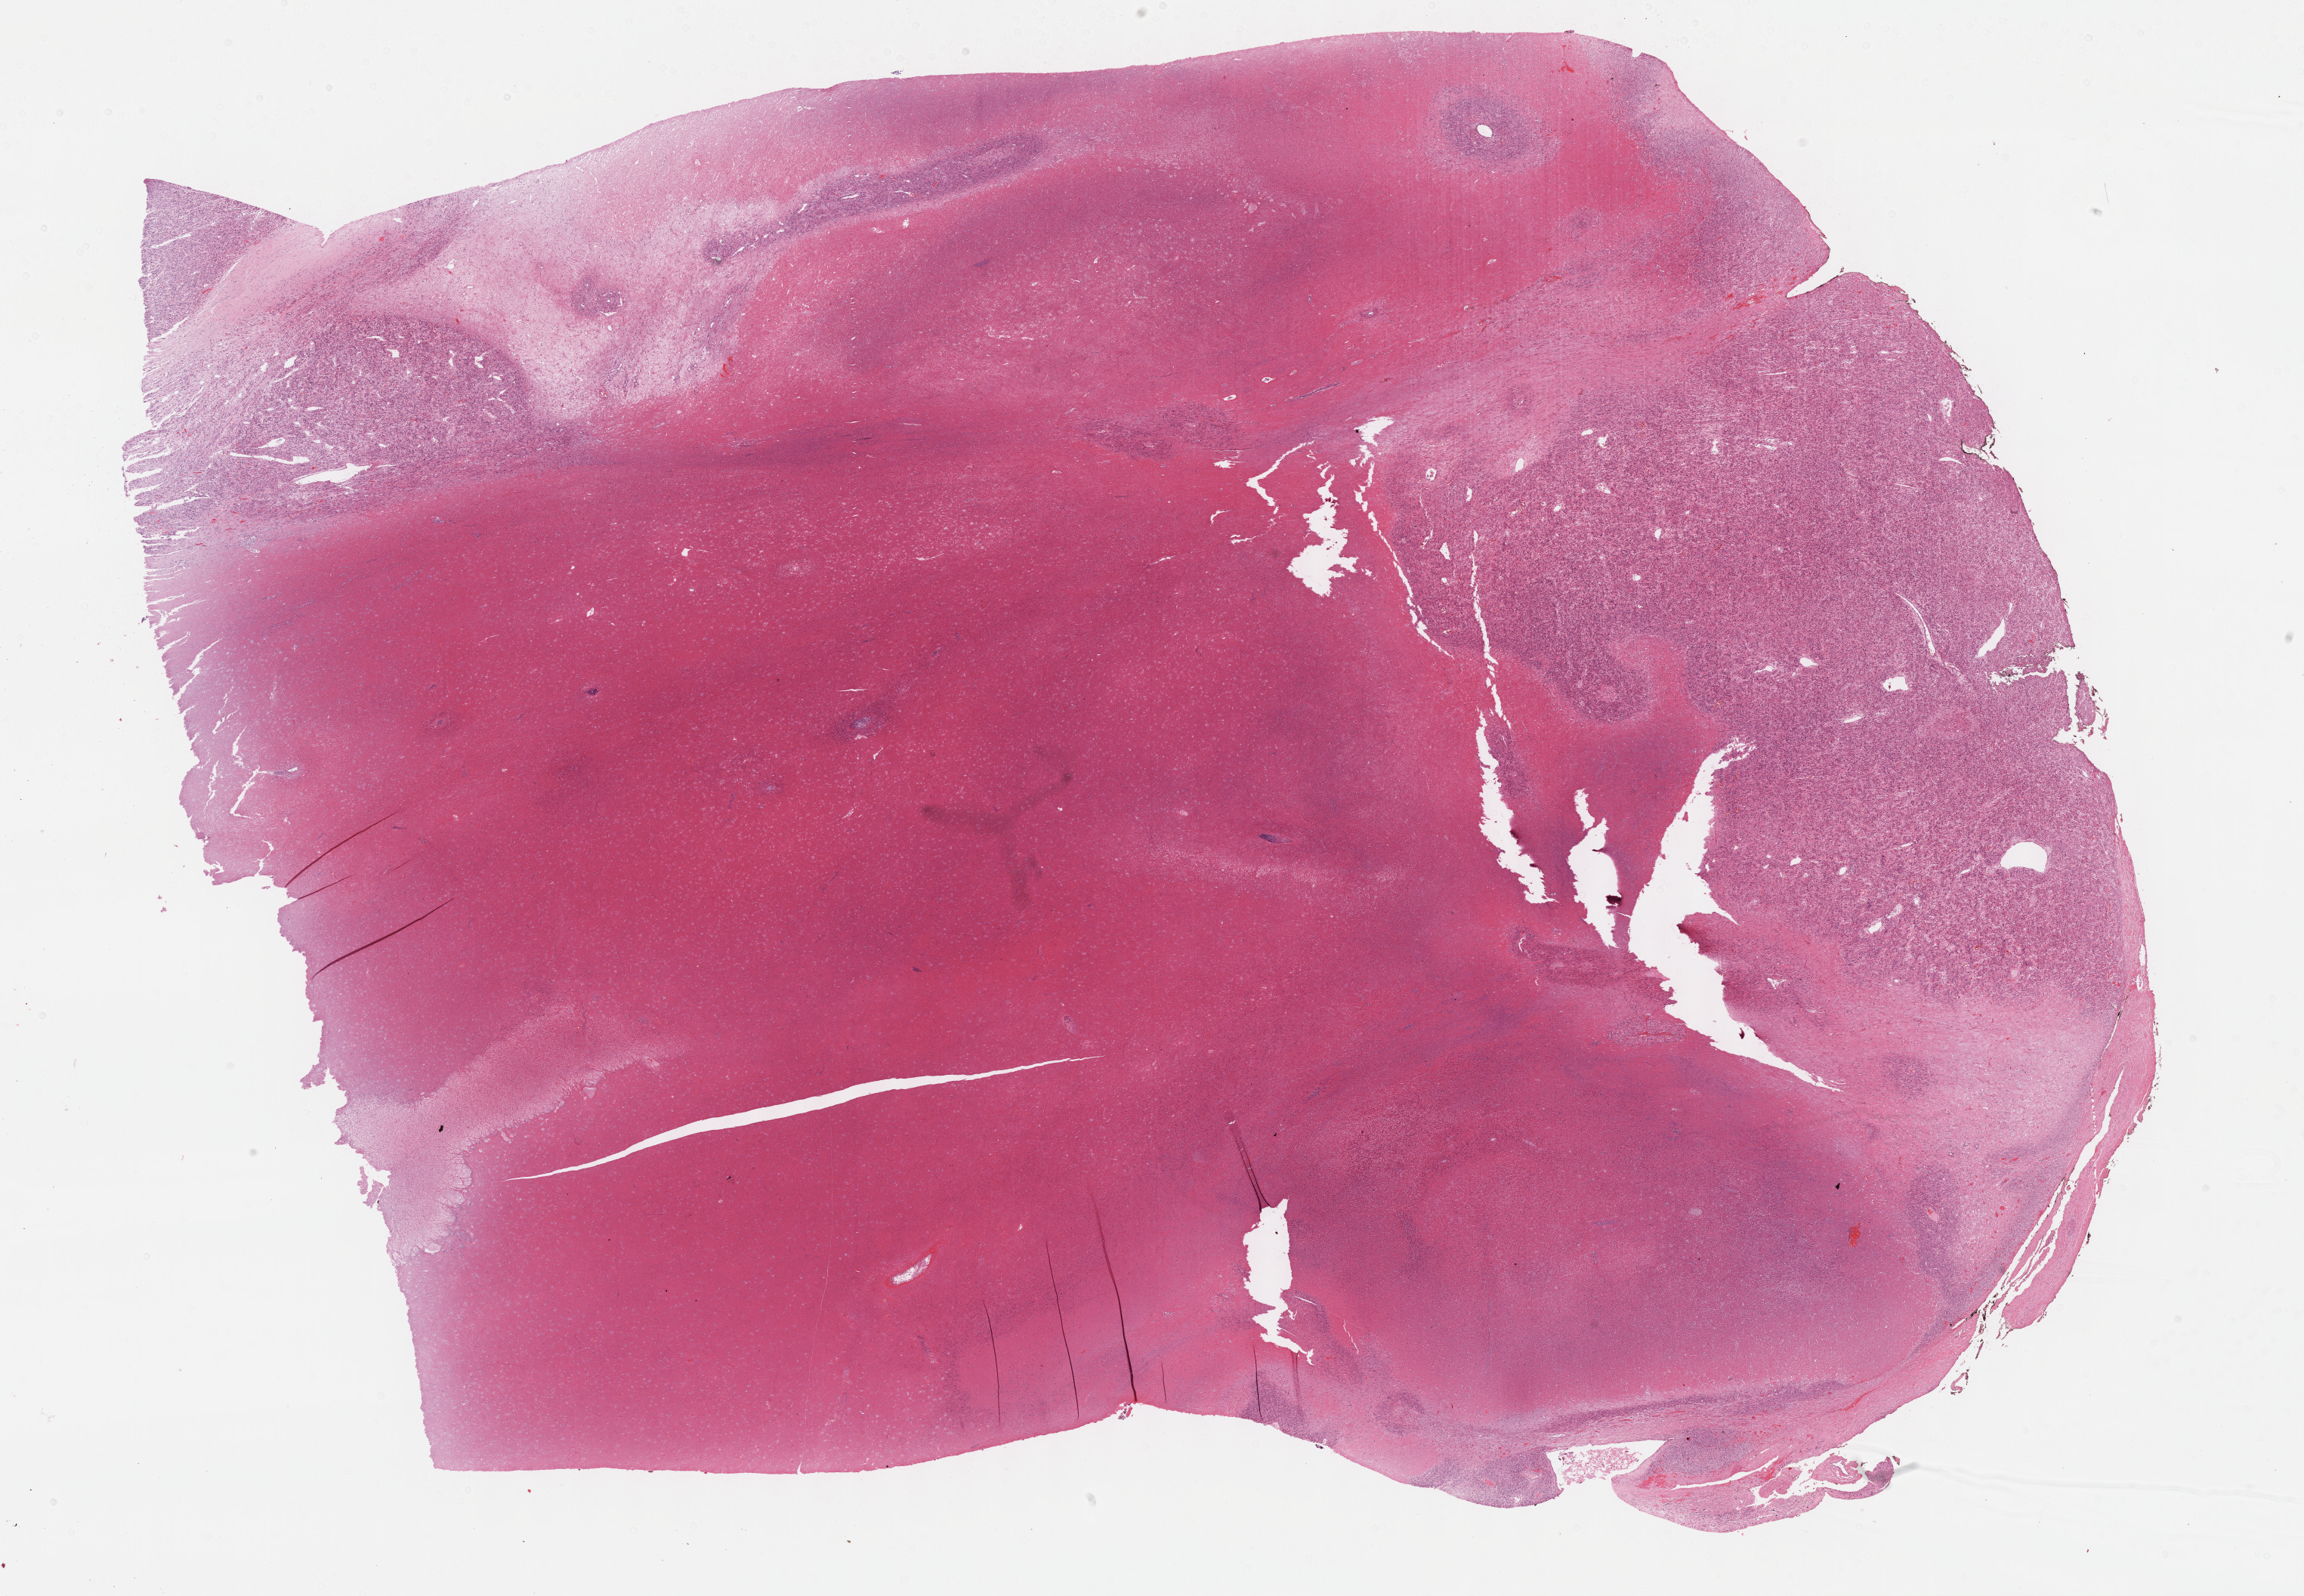
Whole-slide histology image, H&E-stained, a low-resolution overview of the entire scanned area, about 24.7 x 17.1 mm. FFPE section. Sample: primary tumour, retroperitoneum and peritoneum. Patient: female, age at initial diagnosis 53 years.
Pathologic diagnosis: Leiomyosarcoma, NOS (retroperitoneum).